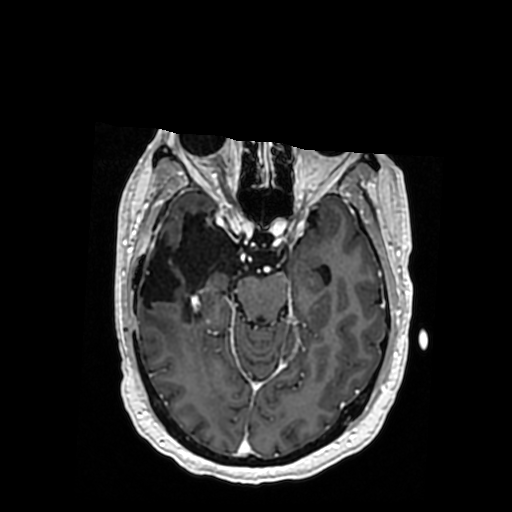
Brain MRI from a brain-tumour surgery series, one axial slice. Slice 220 of 364 in the series (ordered by position). T1-weighted post-contrast. 0.5 mm slice thickness. 512 × 512 image matrix. From the clinical record (not read from this slice): histopathology: Oligodendroglioma; WHO grade: 3; IDH mutation: yes; tumour location: Right Posterior Temporal Inferior Parietal.
Outlined on this slice (manually delineated by an expert):
- previous resection cavity: box from (x=140, y=213) to (x=240, y=320) px